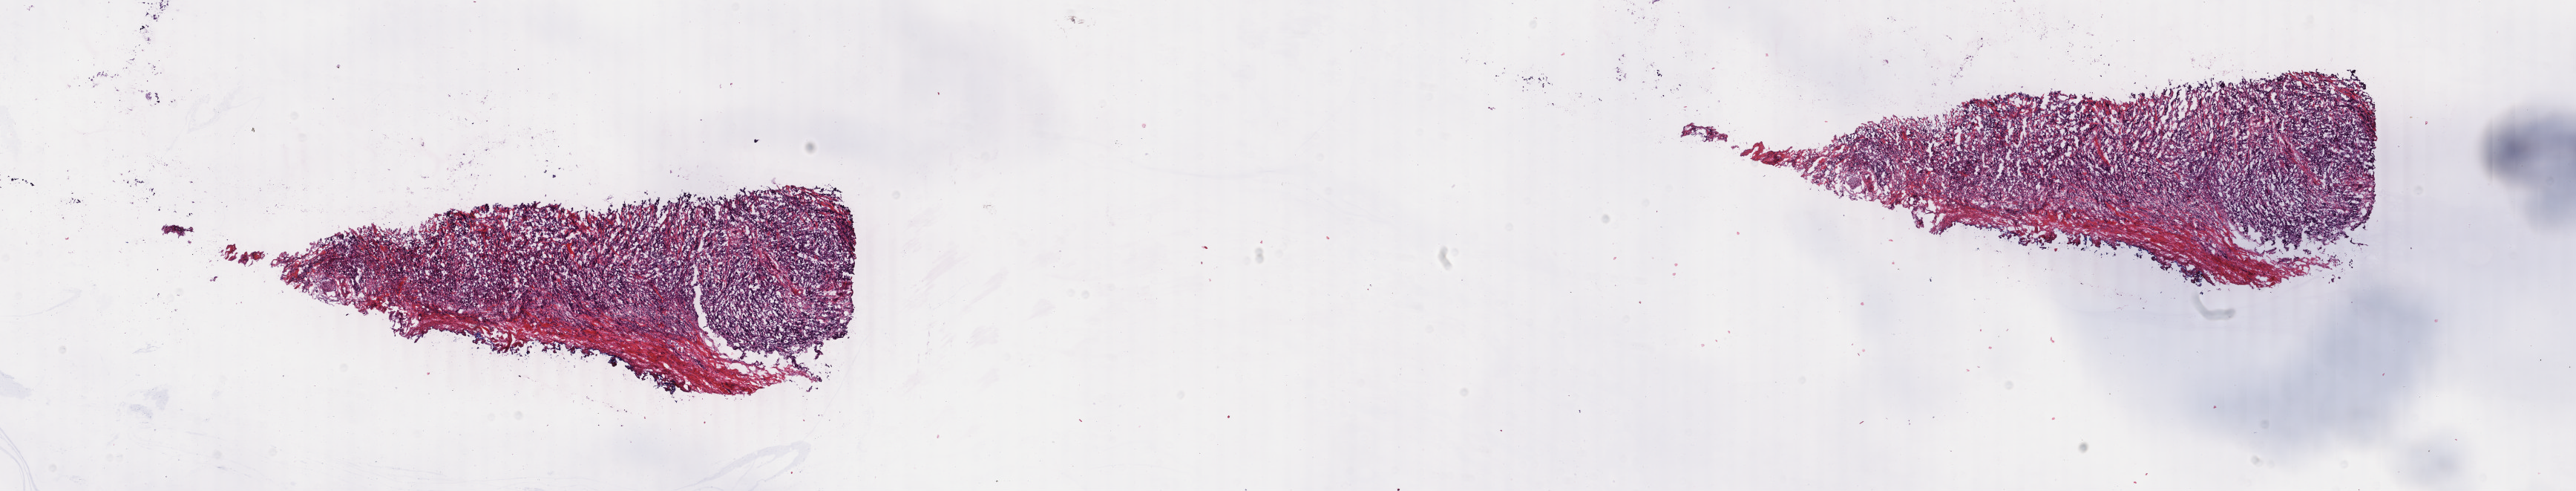
Digitized H&E-stained tissue section (whole slide), a low-resolution overview of the entire scanned area, about 27.6 x 5.3 mm (acquisition: 40x scan), frozen section, sample: primary tumour, breast. Patient: female, age at initial diagnosis 40 years. Pathologist review of this section (percent, as recorded): tumour cells 90%, tumour nuclei 95%, normal cells 0%, stromal cells 10%, necrosis 0%. Infiltration values recorded for this section: lymphocyte infiltration 0%, monocyte infiltration 0%, neutrophil infiltration 0%.
Lymph nodes positive (case pathology): 2 of 23 examined. AJCC pathologic stage: IIB. TNM: T2 N1 M0. Diagnosis: Infiltrating duct carcinoma, NOS.